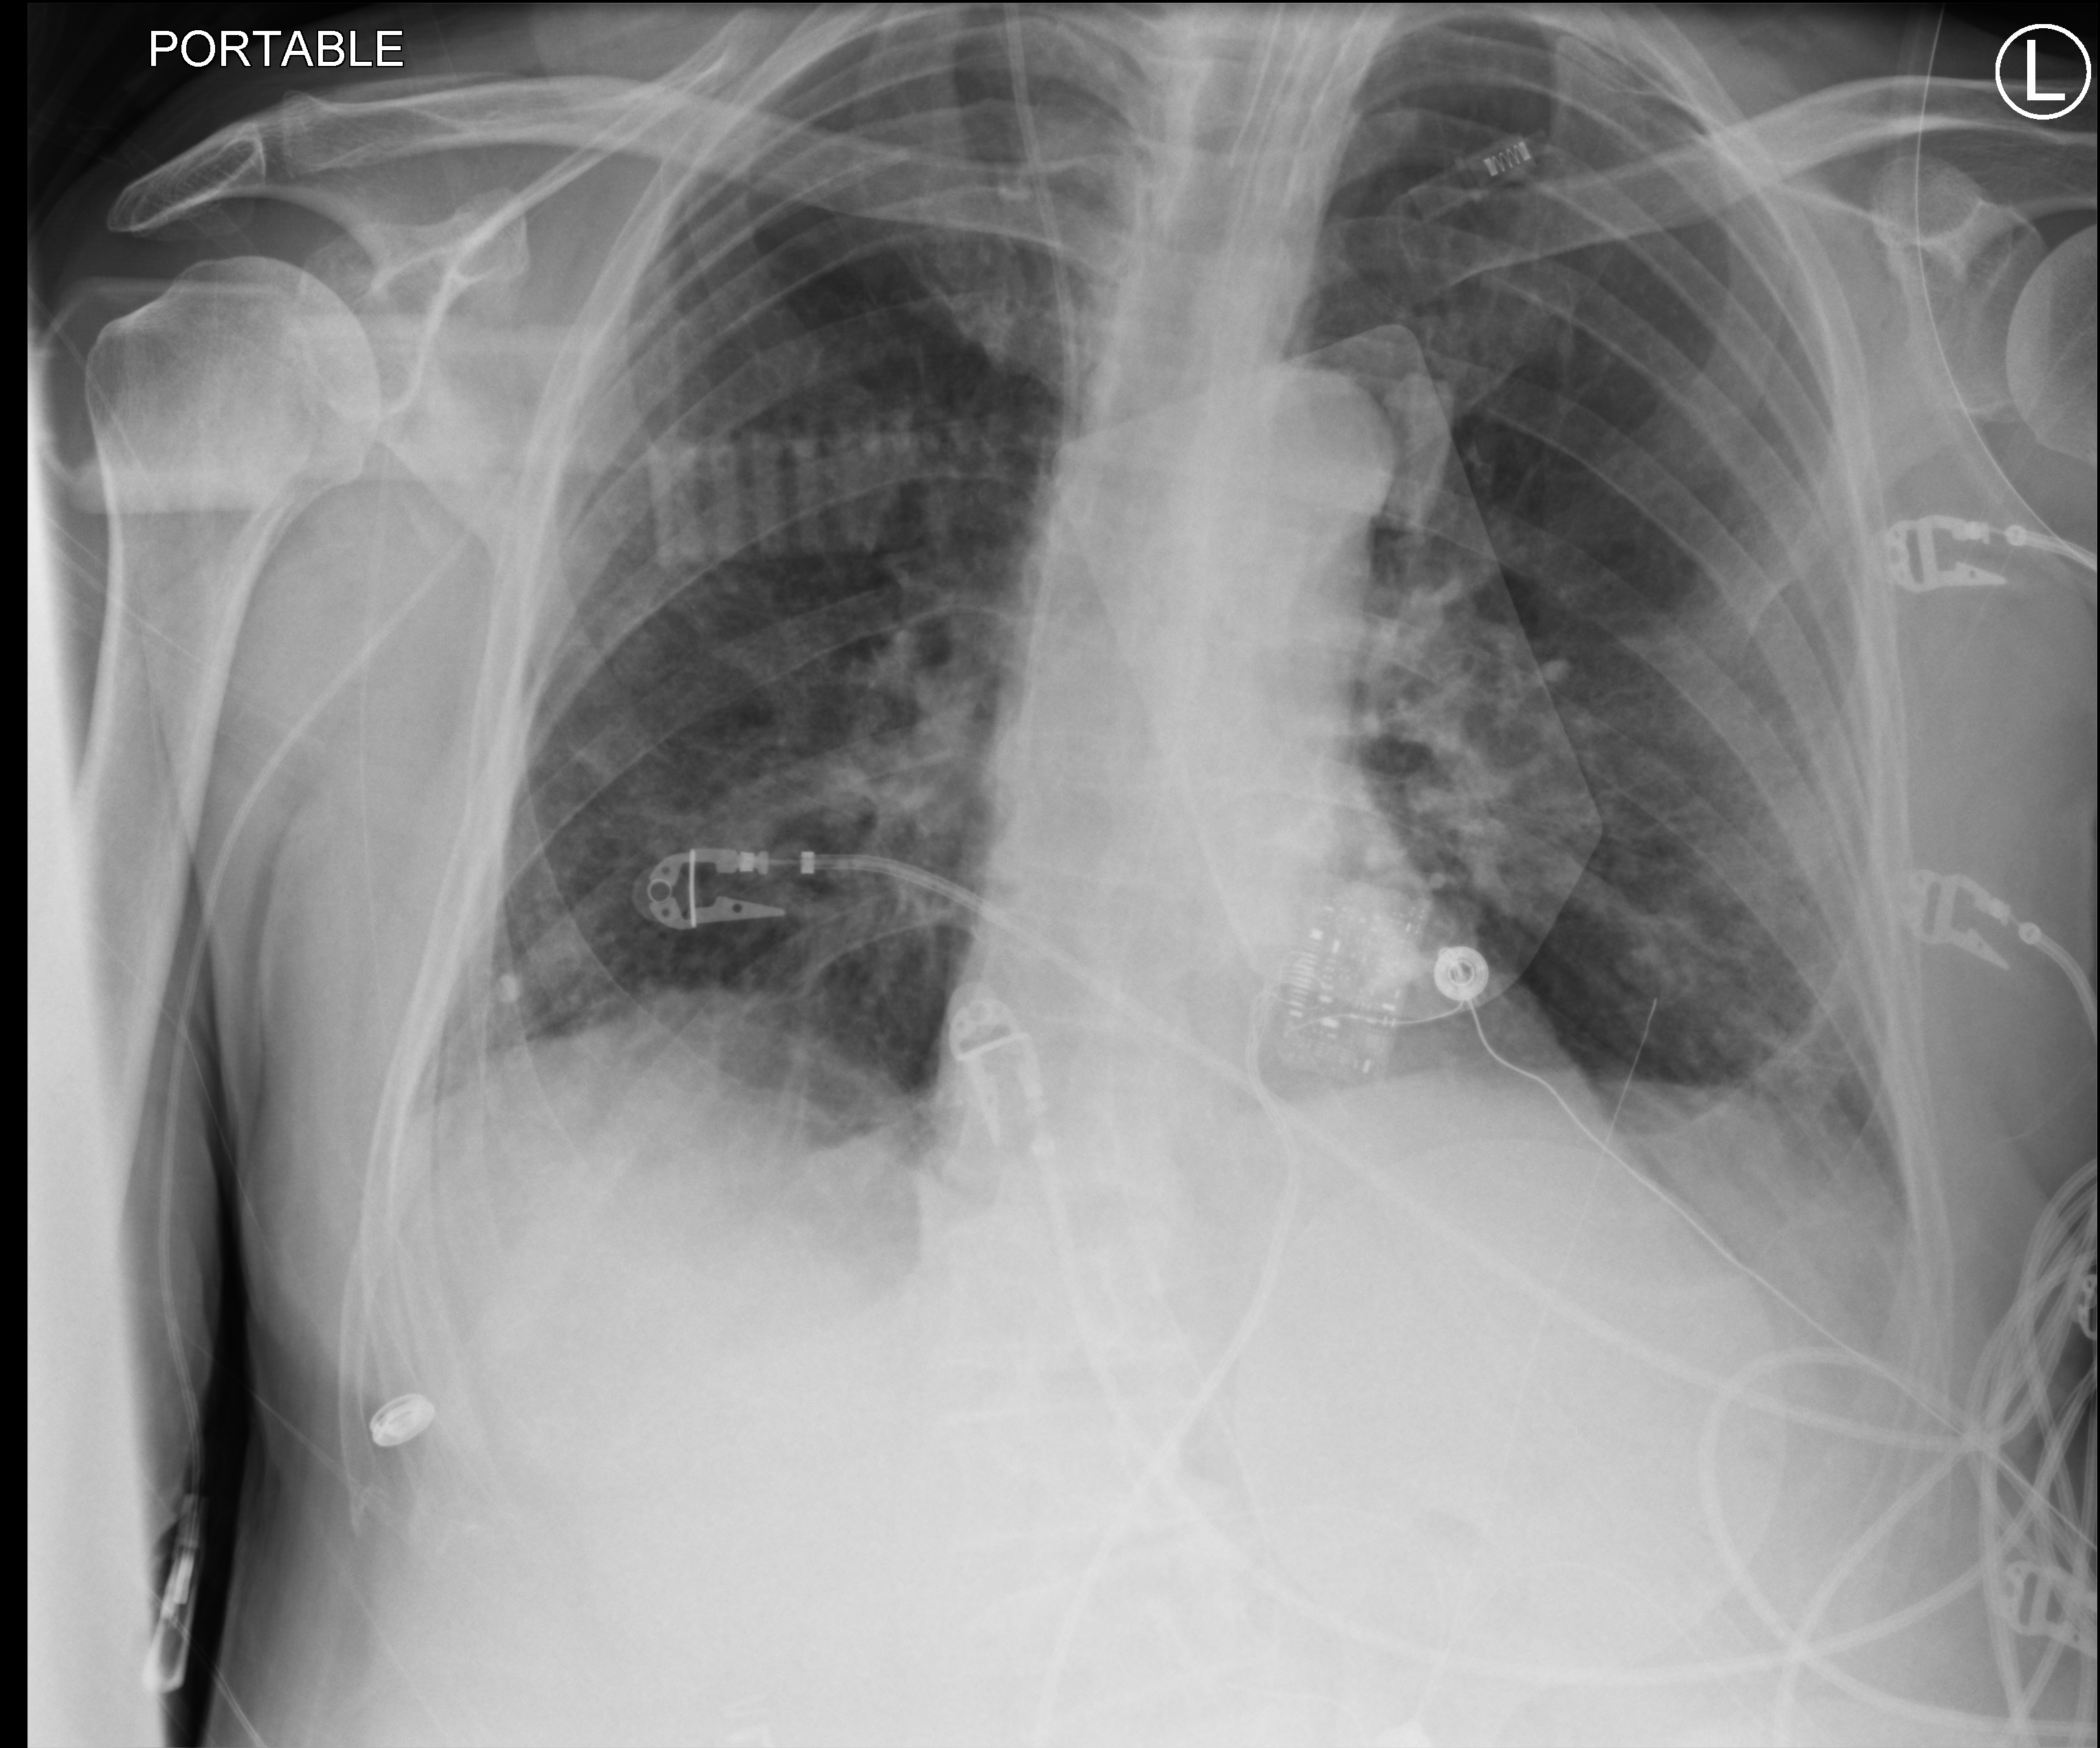
Bedside chest radiograph (computed radiography); anteroposterior (AP) projection. Patient hospitalised with COVID-19; male, aged 75–90 years.
From the hospital-stay record, not from the radiograph (when in the stay this image was taken is not recorded): length of hospital stay: 70 days; smoking status (admission record): never.